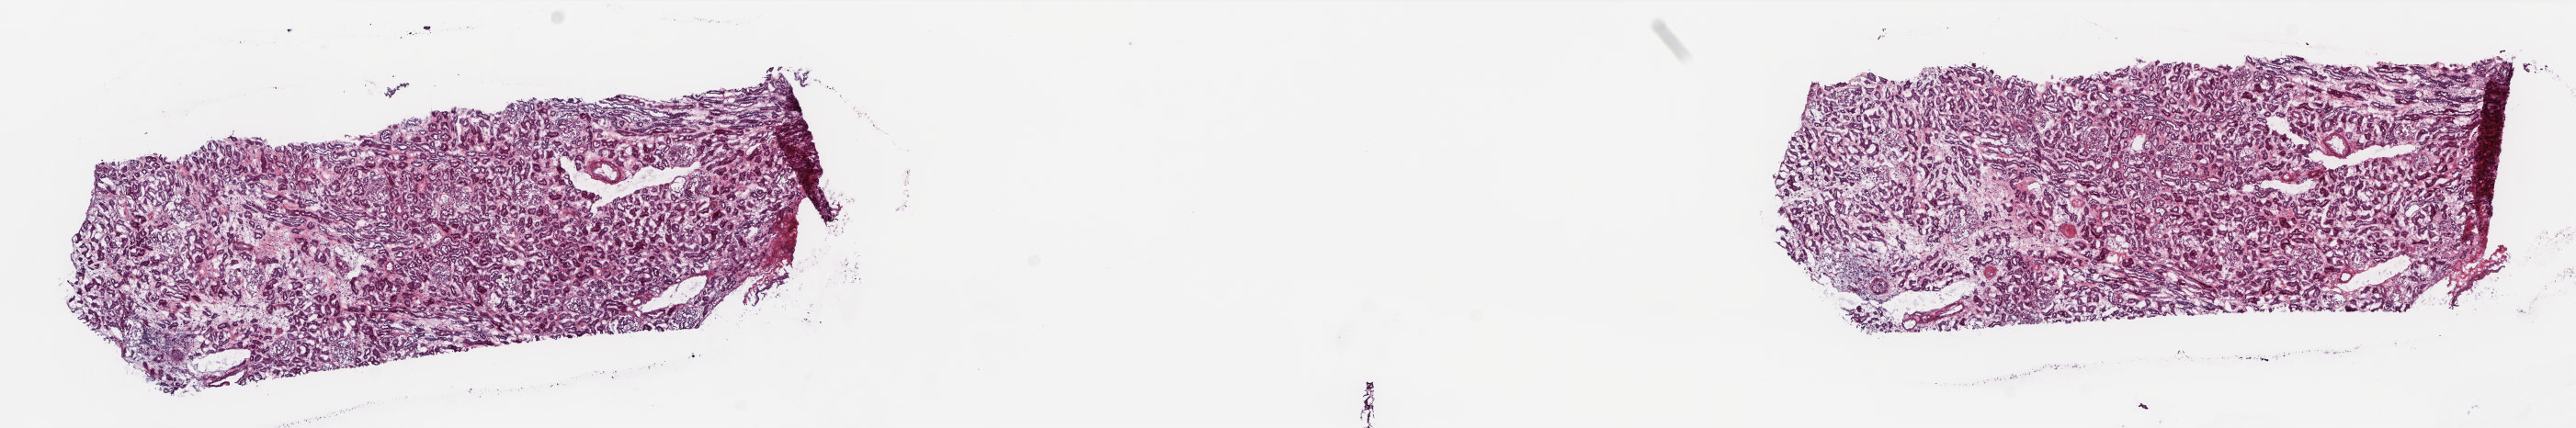
Digitized H&E tissue section (whole slide), shown as a low-resolution overview of the whole scanned area (about 22.6 x 3.8 mm, from a 20x scan). Frozen section. Sample: solid tissue normal (non-tumour tissue), kidney. Female patient; age at initial diagnosis 65 years. Slide review estimates, as recorded: tumour cells 0%, tumour nuclei 0%, normal cells 100%, stromal cells 0%, necrosis 0%. Infiltration values recorded for this section: lymphocyte infiltration 1%, monocyte infiltration 0%, neutrophil infiltration 0%.
This section: solid tissue normal (non-tumour) sample from the same patient. Patient diagnosis: Papillary adenocarcinoma, NOS.